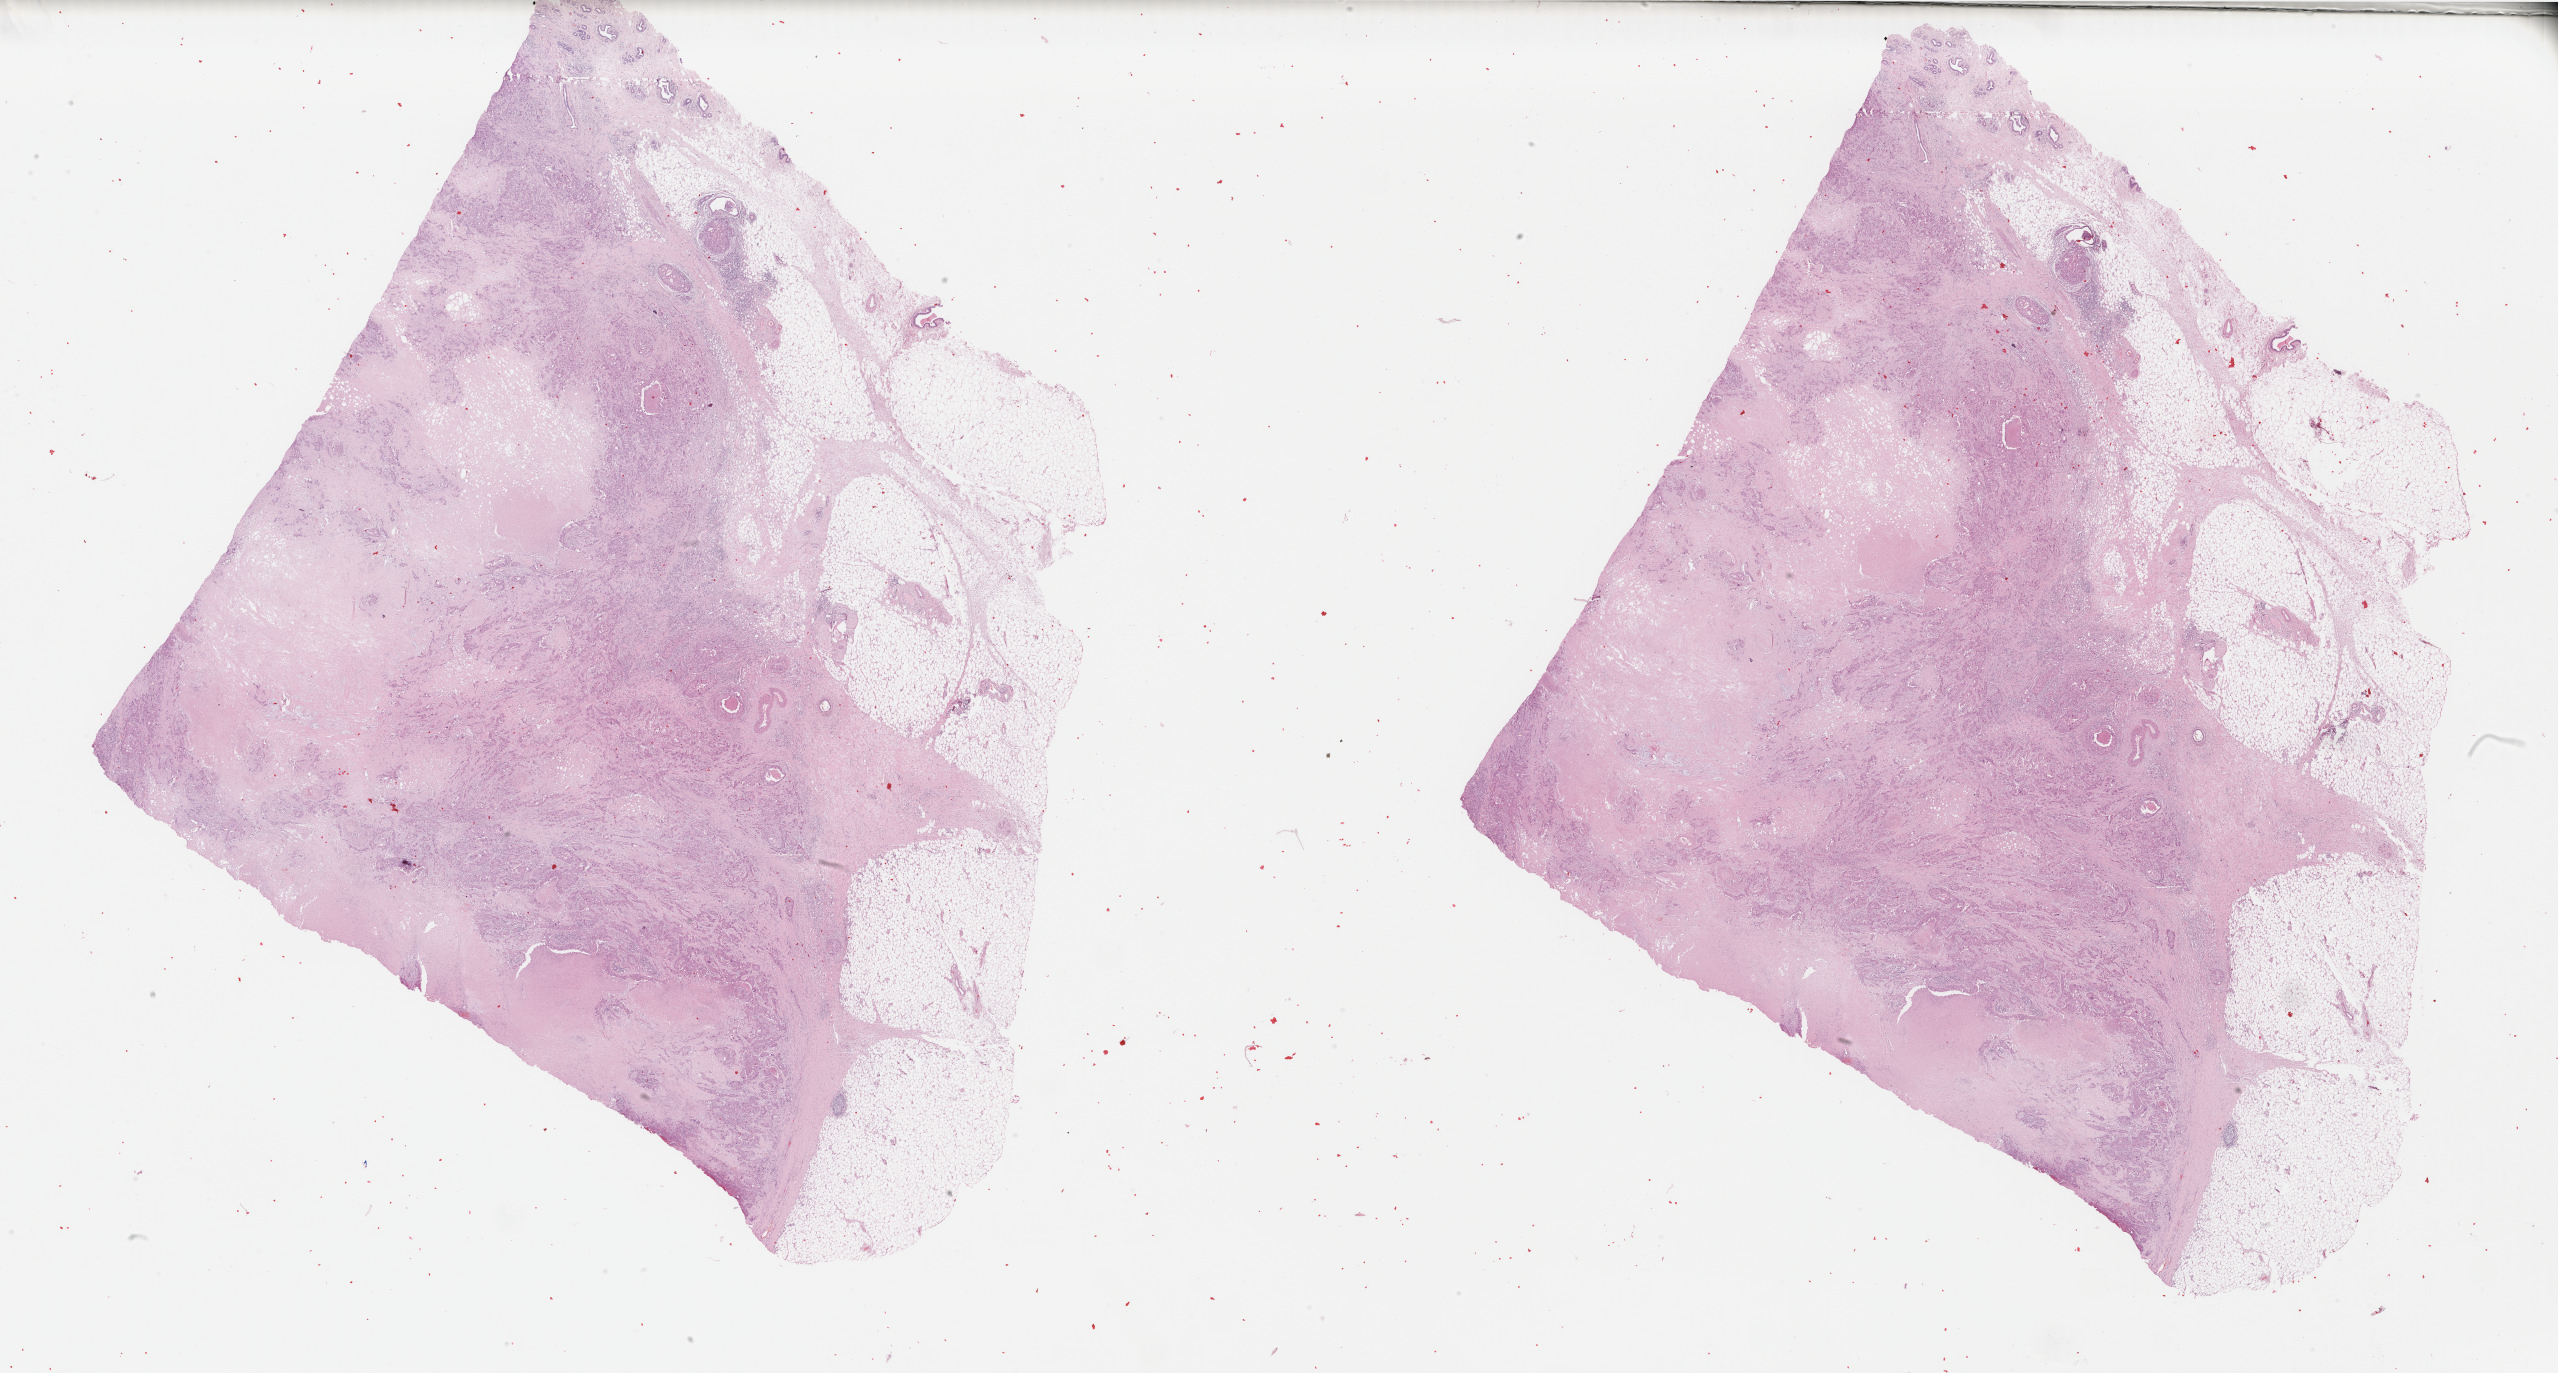
Whole-slide histology image, Hematoxylin and eosin (H&E) stained, a low-resolution overview of the entire scanned area, about 40.6 x 21.8 mm (acquisition: 40x scan). Formalin-fixed paraffin-embedded (FFPE) diagnostic section. Primary tumour sample from the breast. Female patient.
Diagnosis: Infiltrating duct carcinoma, NOS. Lymph nodes positive (case pathology): 0 of 13 examined. AJCC pathologic stage: IIA (7th edition).